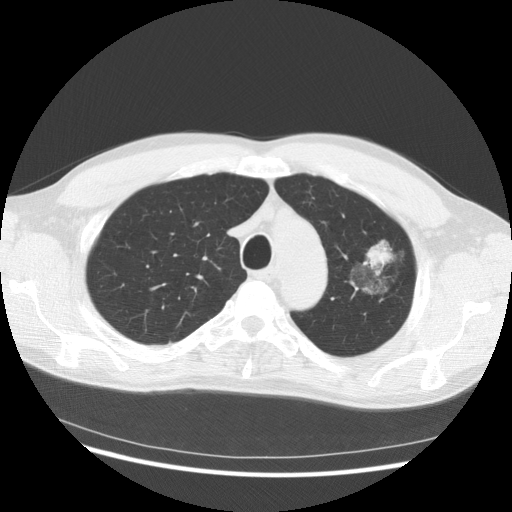
Axial slice from a low-dose chest CT screening exam; third screening round (two years after baseline); lung window (W 1500 / L -600 HU); 512 × 512 image matrix. Male, age 61 years at enrolment.
Lesion marked by an expert reader, bounding box <331,237,406,317> (left, top, right, bottom; pixels). Reader record for this screening exam (exam-level; its link to the box is not recorded): non-calcified nodule or mass ≥4 mm, left upper lobe, 37 × 33 mm, poorly defined margins, mixed attenuation, pre-existing on the prior screen: yes; interval growth: yes. Official screen result: positive, other. Participant outcome: lung cancer diagnosed 361 days after this screen — bronchiolo-alveolar adenocarcinoma, NOS, left upper lobe, well differentiated (G1), stage IB (AJCC 6th edition), 44 mm at pathology.